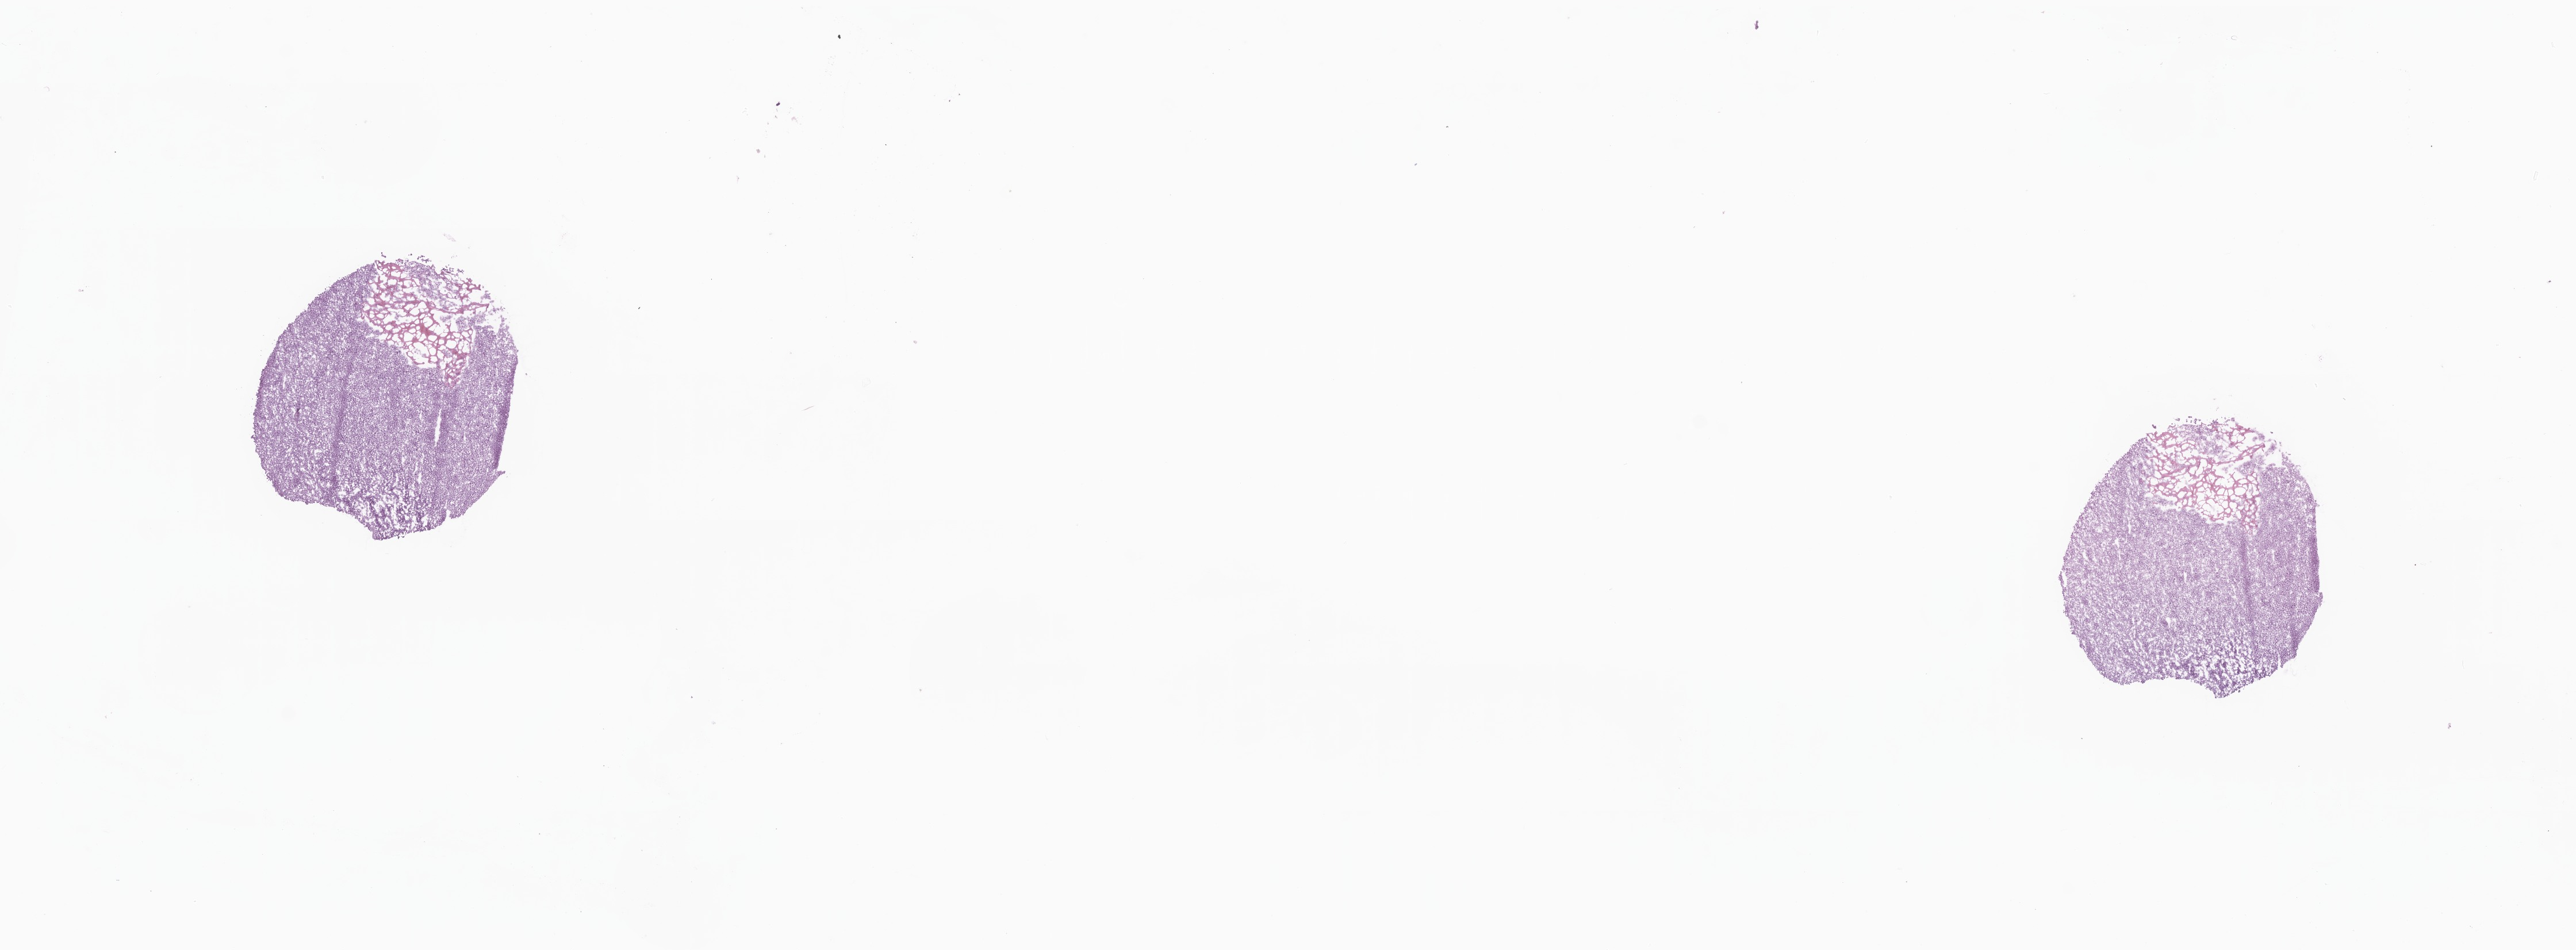
Digitized H&E-stained section, whole scanned area (about 18.9 x 7.0 mm) shown as a low-resolution overview. Cryosection. Metastatic tumor tissue, resected from pleura. Patient: male, age at initial diagnosis 55 years. Pathologist review of this section (percent, as recorded): tumor cells 90%, tumor nuclei 90%, stromal cells 10%, necrosis 0%, normal cells 0%. Inflammatory infiltration, as recorded: lymphocyte infiltration 4%, monocyte infiltration 1%, neutrophil infiltration 2%.
• section: top of the tissue portion
• patient diagnosis (primary): Adenocarcinoma, NOS